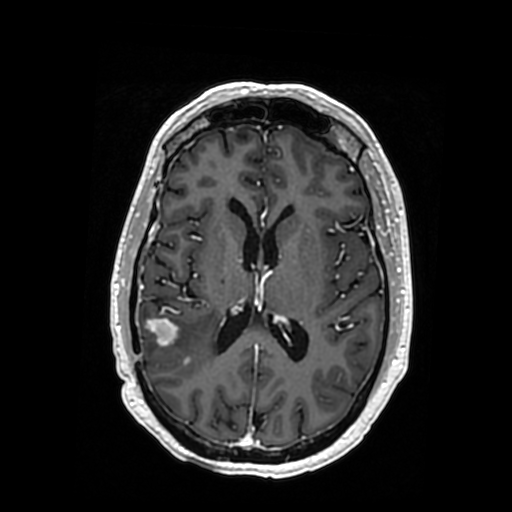
Brain MRI from a brain-tumour surgery series, one axial slice. T1-weighted post-contrast. 512 × 512 image matrix. From the clinical record (not read from this slice): histopathology: Oligodendroglioma; WHO grade: 3; IDH mutation: yes; tumour location: Right Posterior Temporal Inferior Parietal.
Outlined on this slice (outlined manually by an expert reader):
- tumour: box from (x=171, y=318) to (x=216, y=364) px